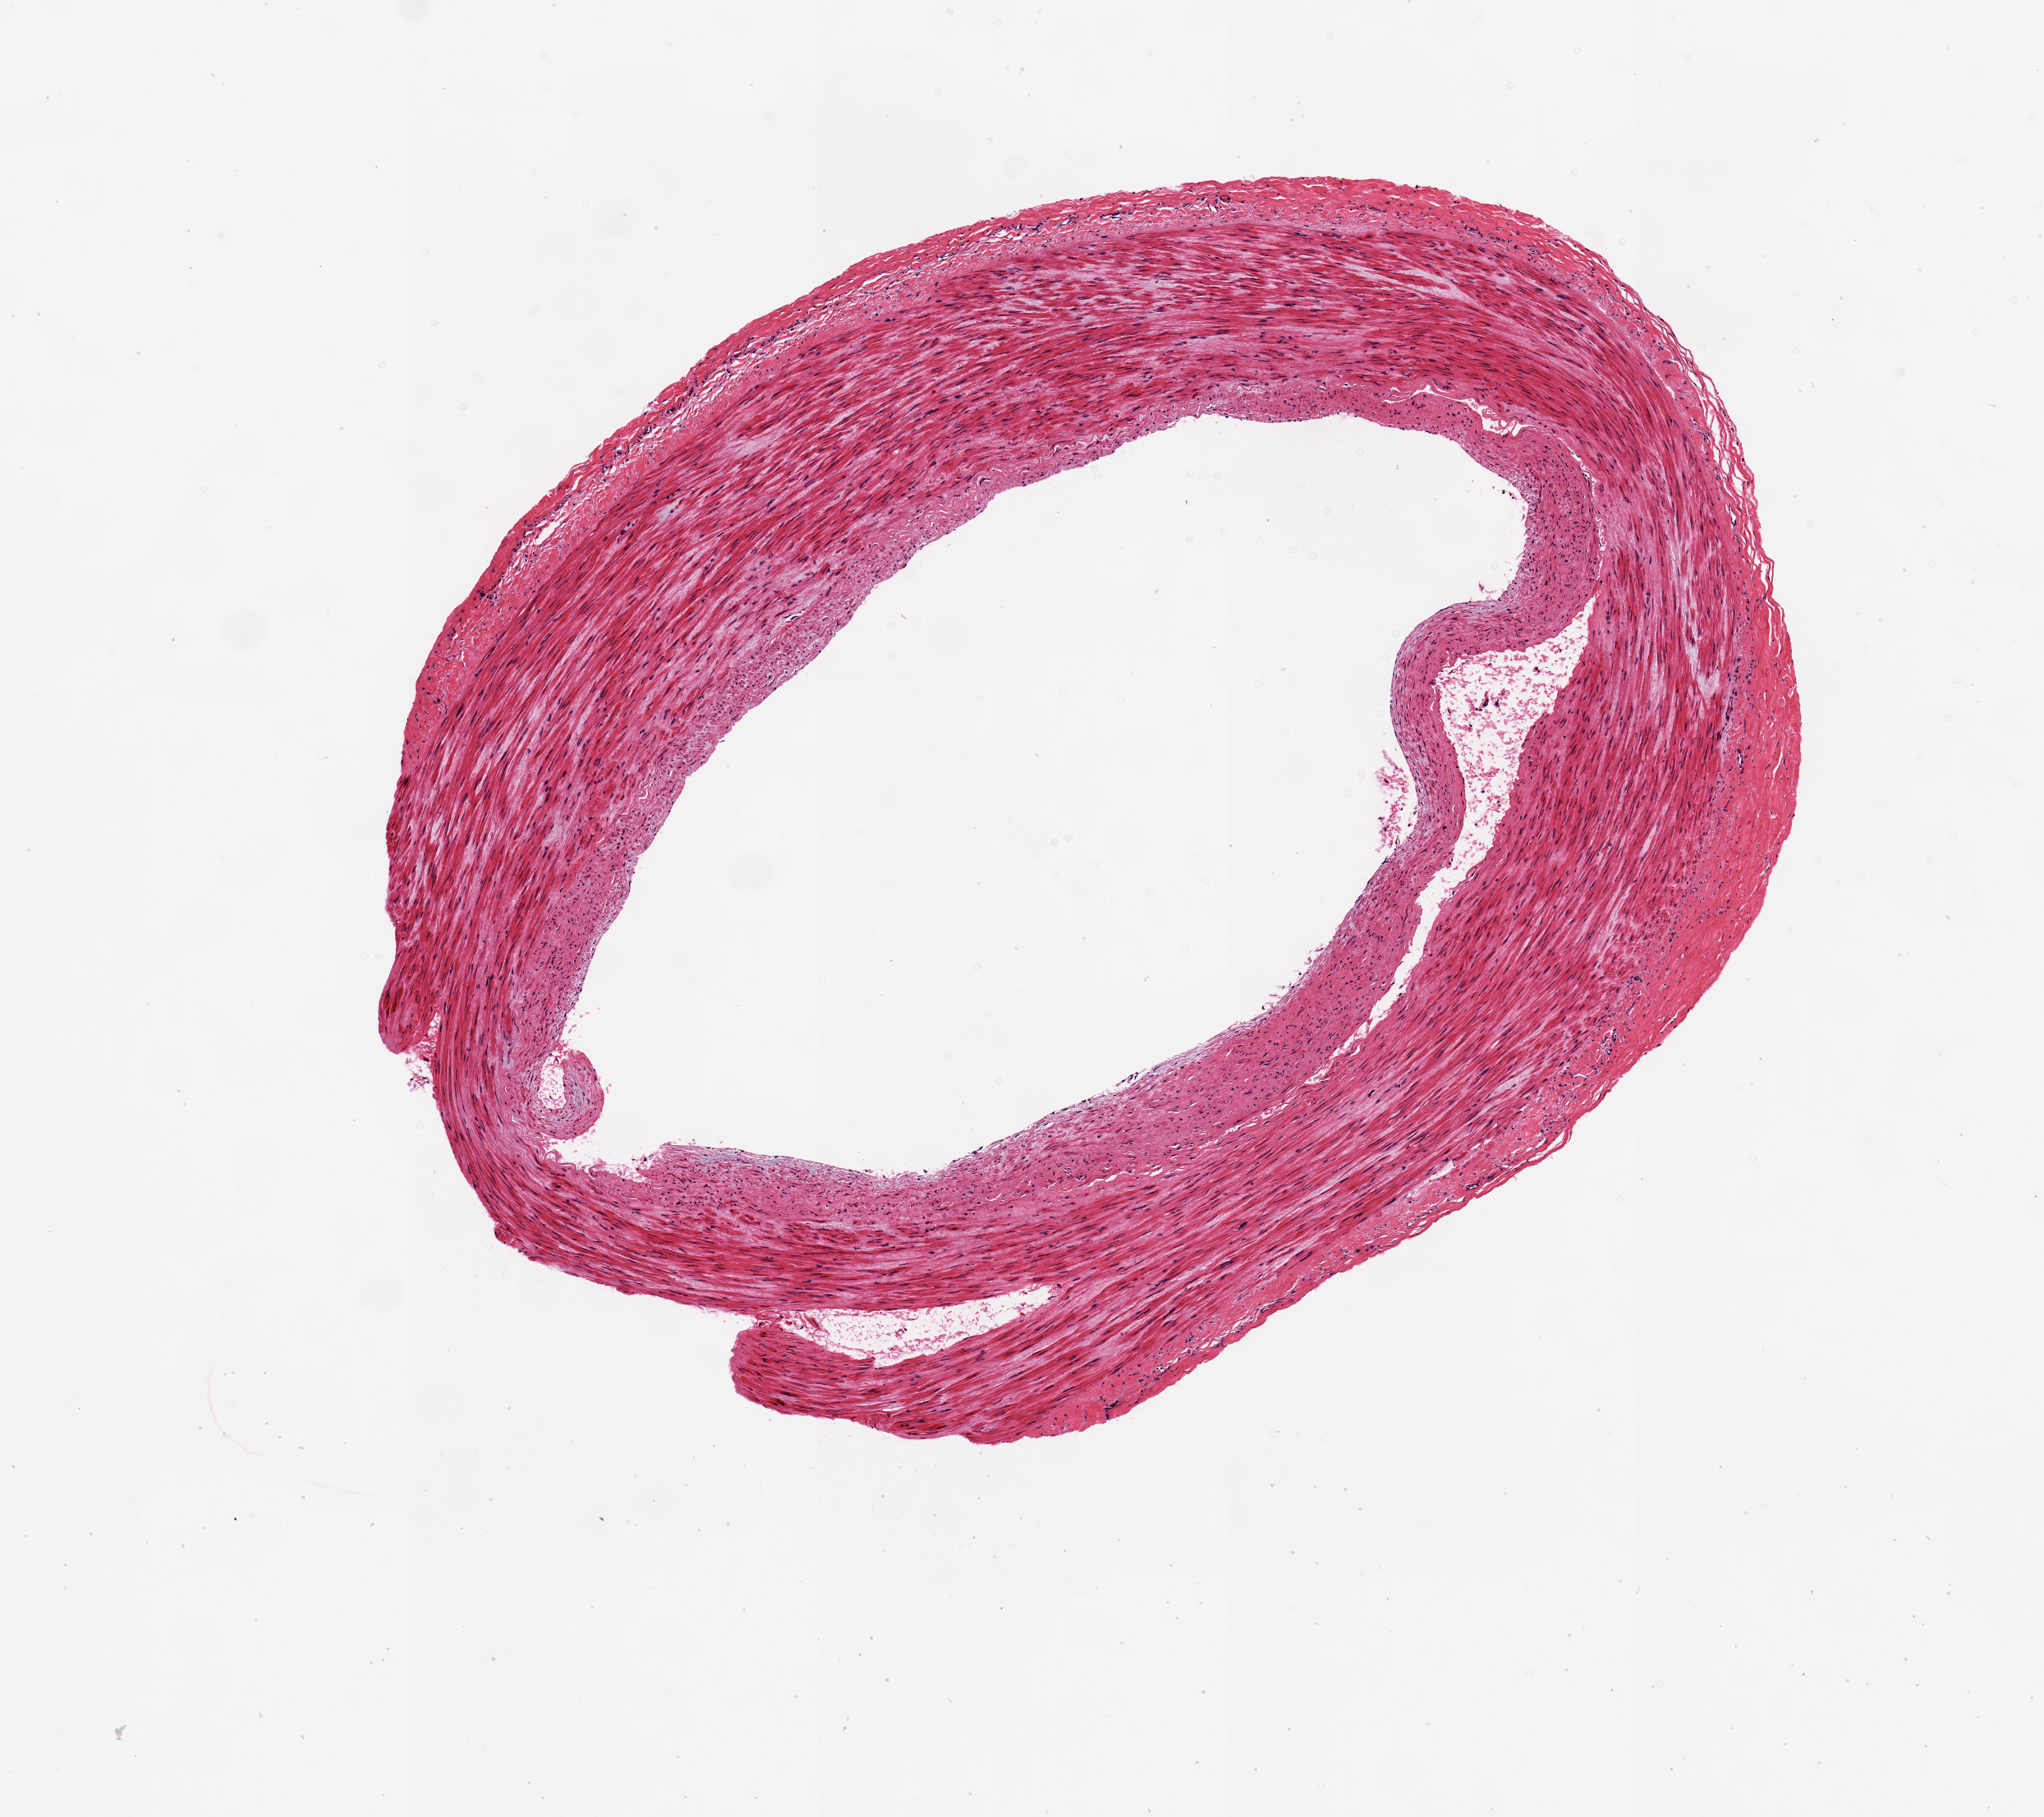
Digitized H&E-stained section, low-resolution overview of the scanned area, about 4.9 x 4.4 mm. PAXgene-fixed paraffin-embedded (PFPE) section. Section of tibial artery (target tissue). Donor tissue sample. Male donor.
Review note (as recorded): OK for analysis.